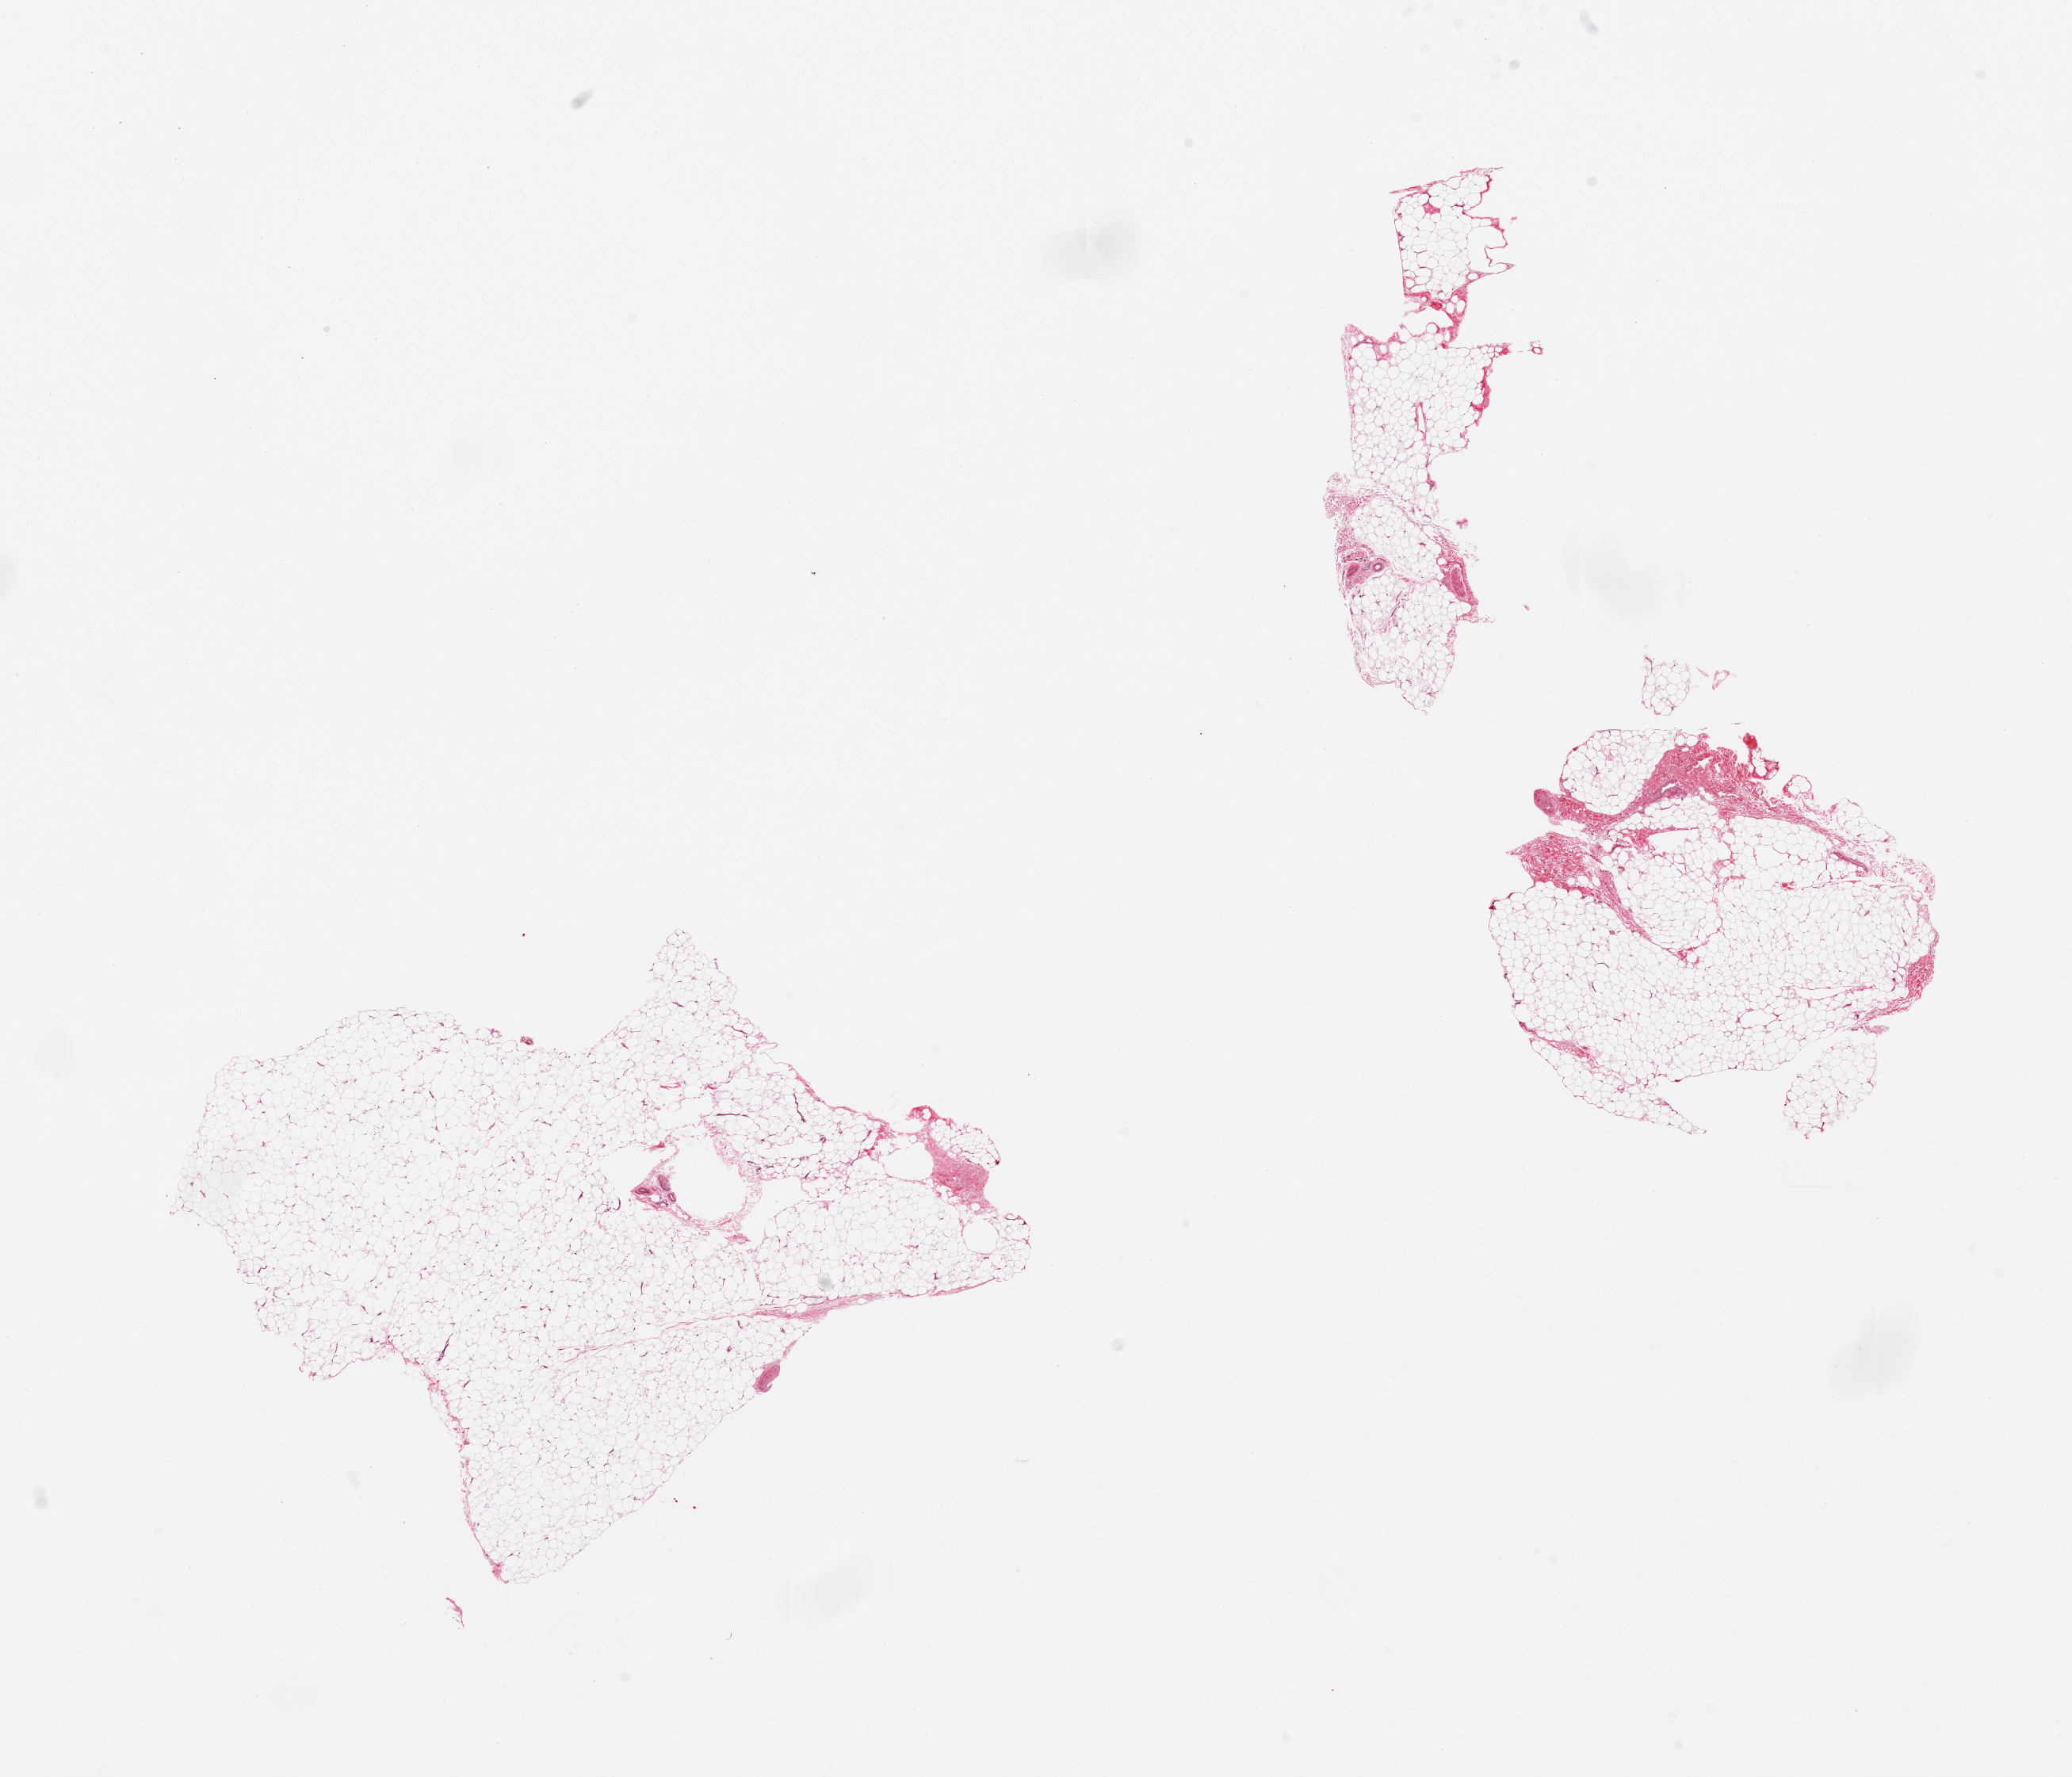
Digitized hematoxylin and eosin (H&E)-stained section, brightfield, low-resolution overview of the scanned area, about 20.7 x 17.7 mm (from a 20x scan). PAXgene-fixed, paraffin-embedded tissue. Section of adipose tissue (target tissue). Tissue donor sample.
Reviewer comment on this tissue sample: 3 small irregular pieces.